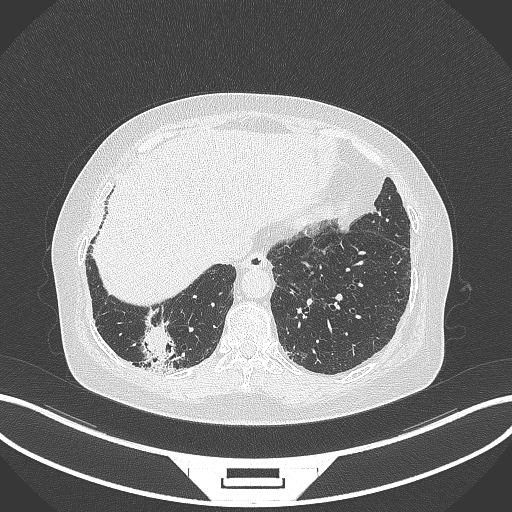
Chest CT, one axial slice. Slice 32 of 296 in the series (ordered by position). Reconstruction kernel B70f. 120 kVp. Lung window (W 1500 / L -600 HU). 512 × 512 image matrix, field of view 400 × 400 mm. Female patient, age 65 years. From the clinical record (not read from this slice): clinical TNM (as recorded): T2b N1 M0.
Annotated regions visible in this slice (rectangle marked by the reading radiologist):
- lung tumour (recorded histology: adenocarcinoma): box from (x=140, y=316) to (x=179, y=374) px